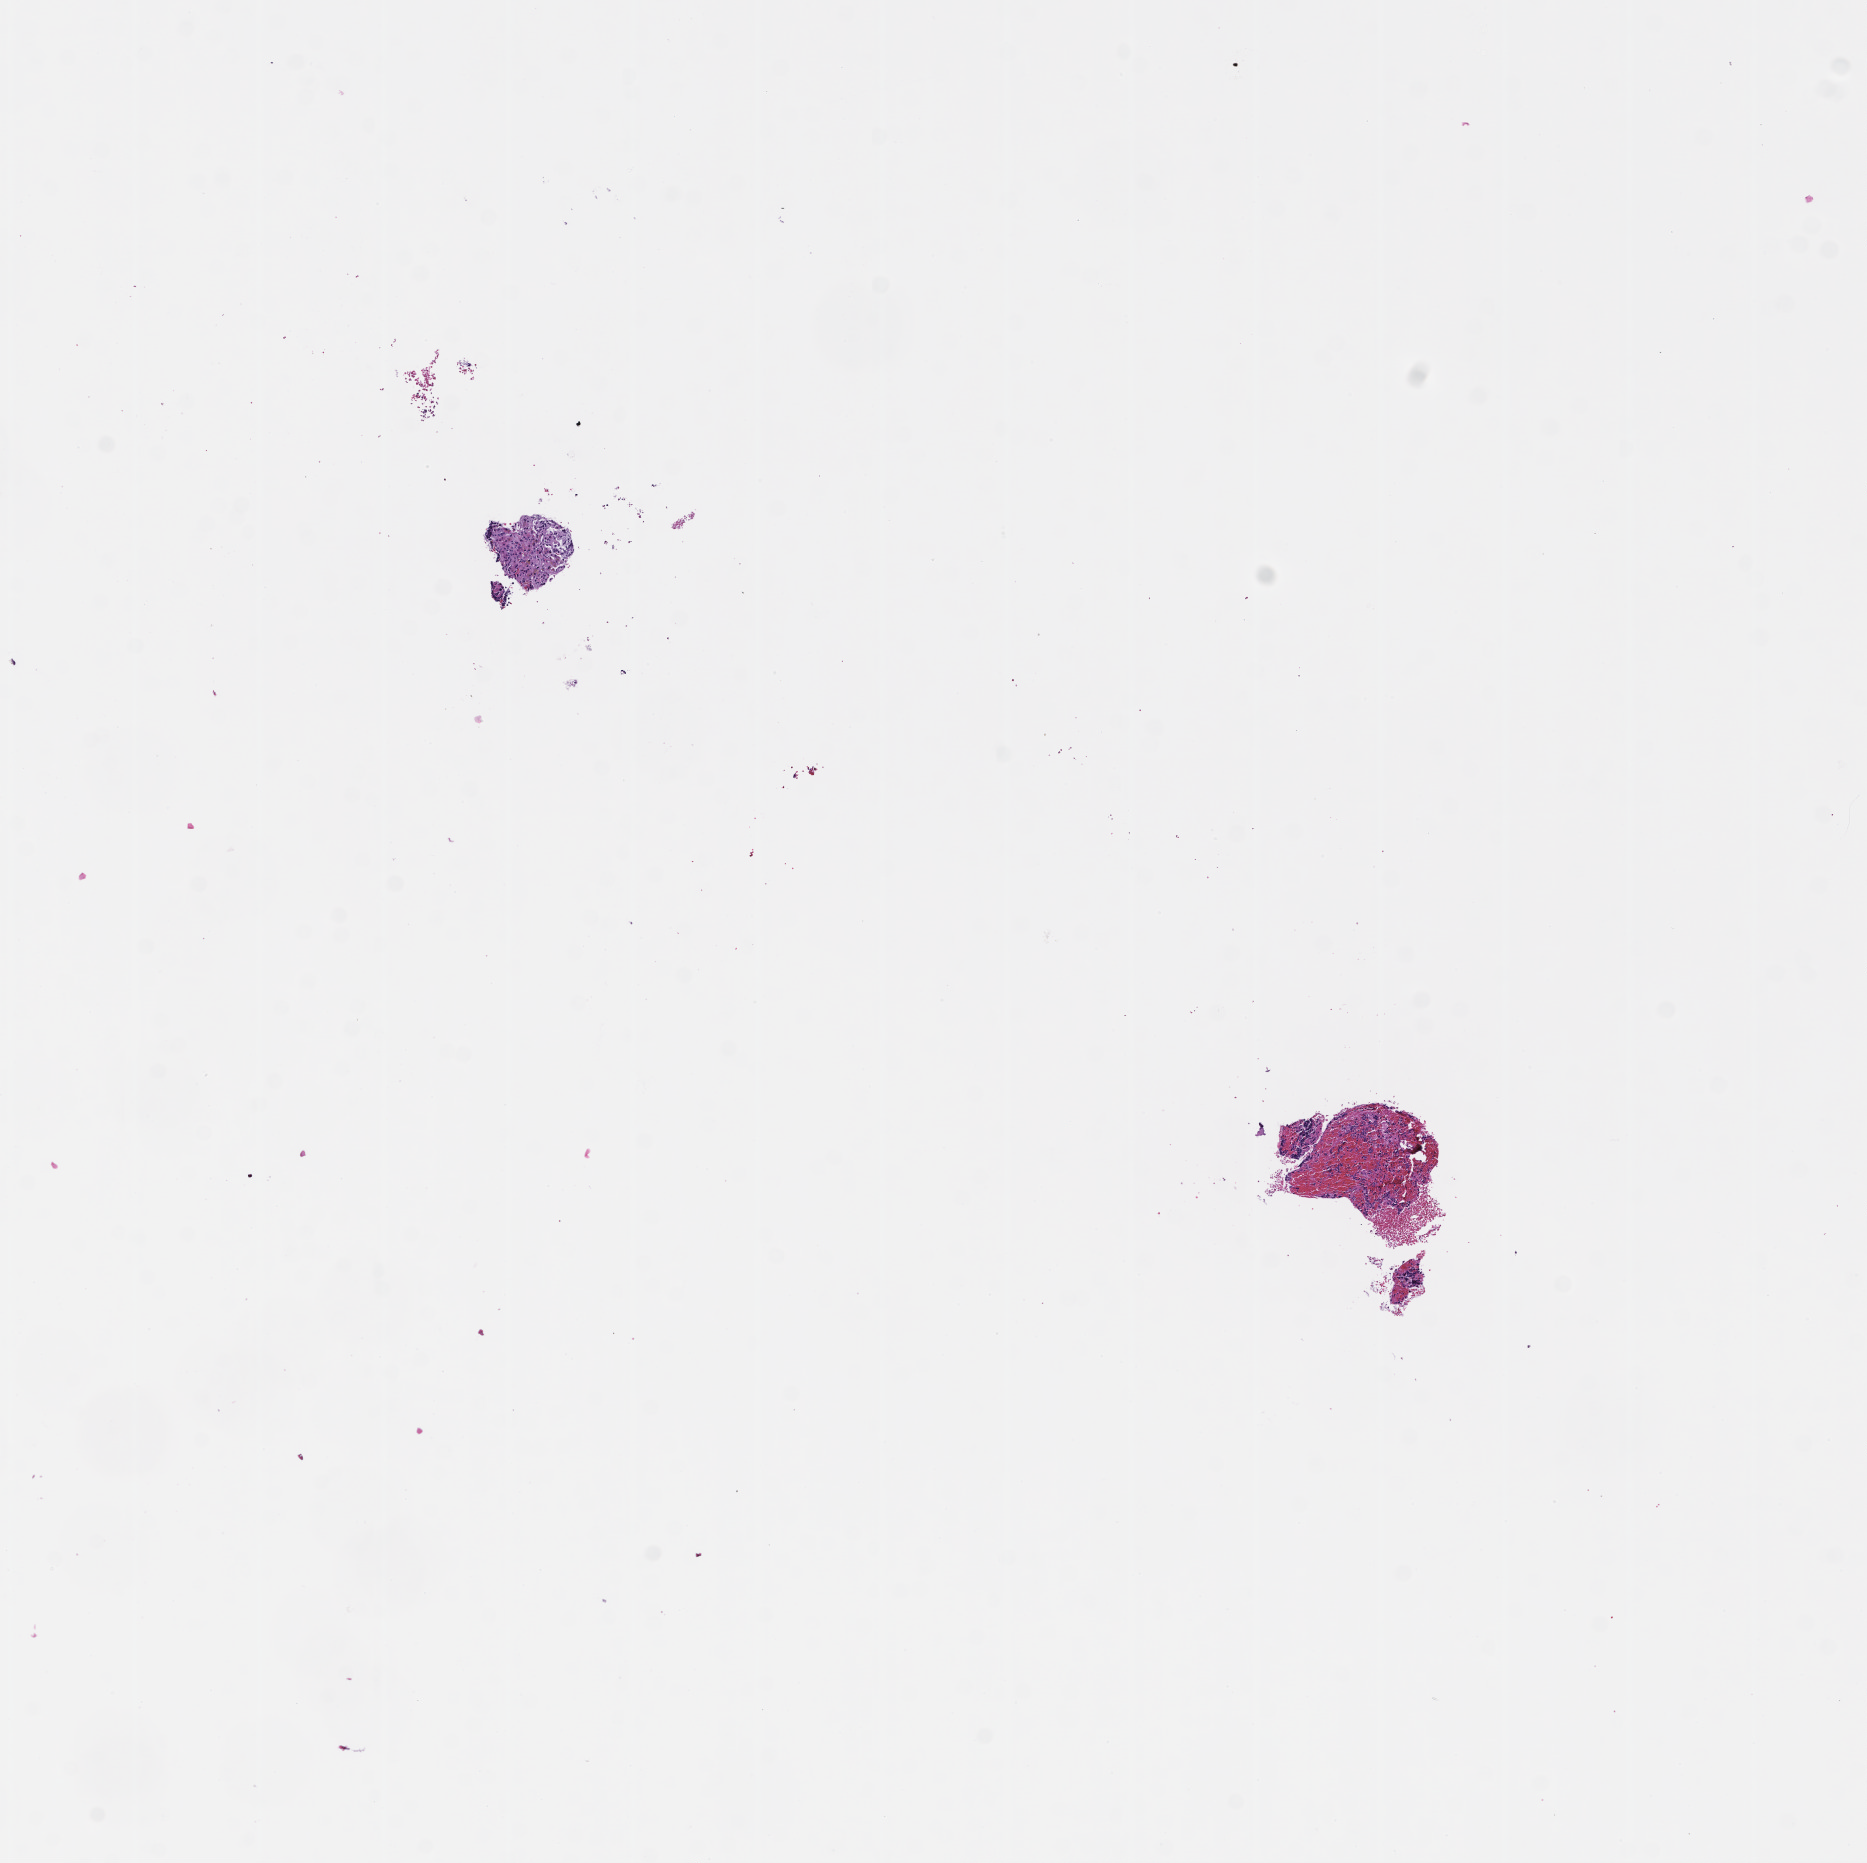
Digitized haematoxylin and eosin-stained section, low-resolution overview of the scanned area, about 7.5 x 7.5 mm. FFPE section. Specimen time point: collected at baseline (before treatment). Female patient.
This section: metastatic tumor tissue. Primary diagnosis of the patient: Adenocarcinoma of the Gastroesophageal Junction.